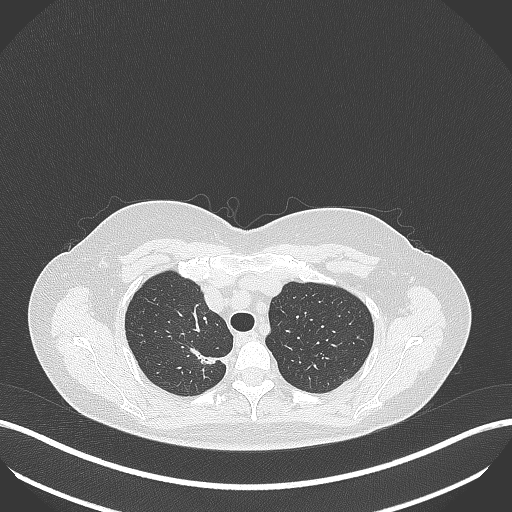
Chest CT, one axial slice; position 319 of 386 along the scan axis; lung window (W 1500 / L -600 HU); 1 mm slice thickness; 512 × 512 image matrix. Patient: female, 65 years. Case-level facts recorded for this patient, not image findings: clinical TNM (as recorded): T1b N0 M0; histopathological grade: G2.
Structures marked on this image (rectangle marked by the reading radiologist):
- lung tumour (recorded histology: adenocarcinoma): bounding box (x1, y1, x2, y2) in pixels: (187, 342, 232, 373)